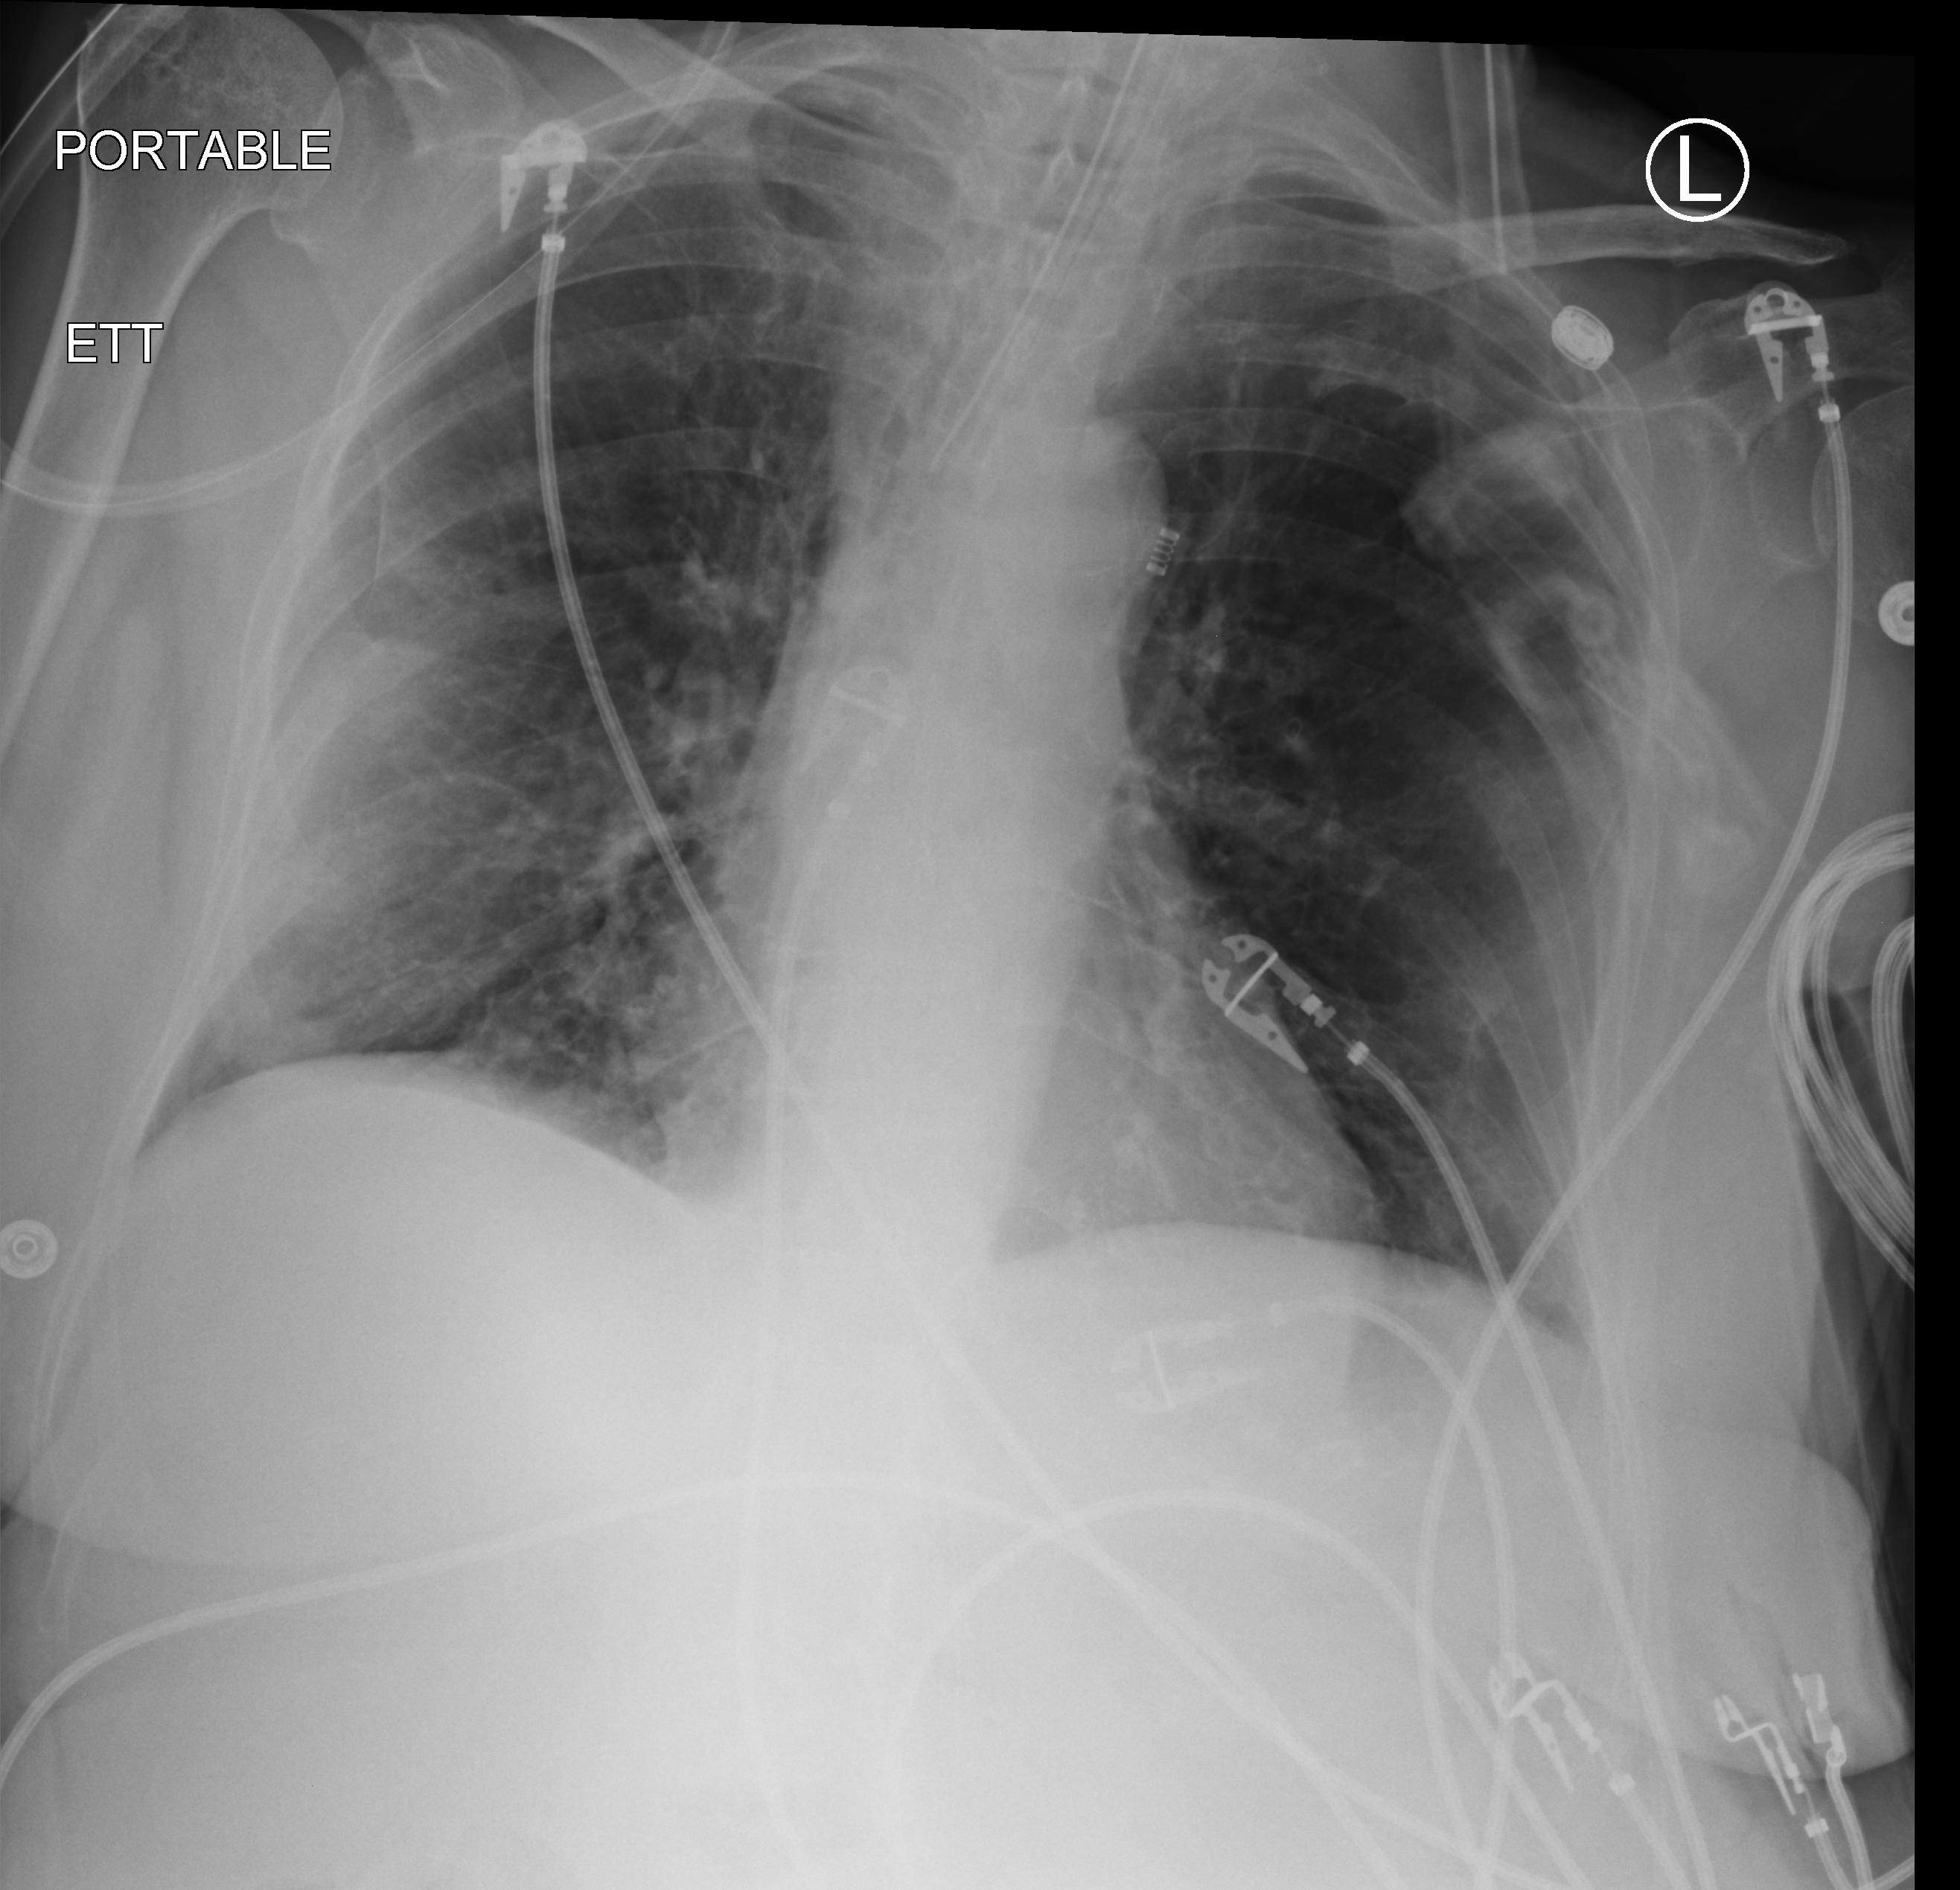
Chest X-ray (portable), anteroposterior (AP) projection. Patient hospitalised with COVID-19; female, aged 75–90 years.
From the hospital-stay record, not from the radiograph (when in the stay this image was taken is not recorded): chronic kidney disease (admission record): yes.